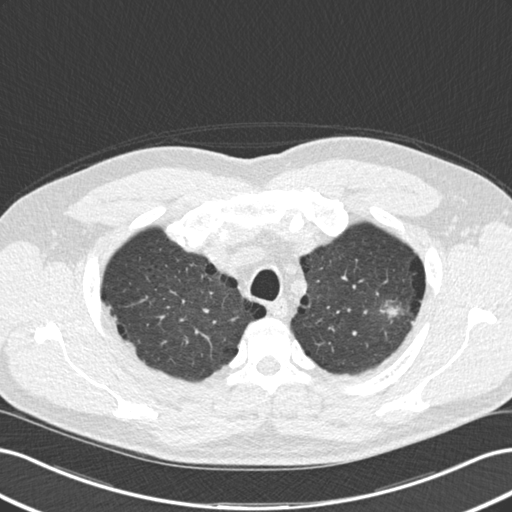
Low-dose screening chest CT, one axial slice. Slice 139 of 177 in the series (ordered by position). Reconstruction kernel B30f. 120 kVp. Lung window (W 1500 / L -600 HU). 2 mm slice thickness. 512 × 512 image matrix.
Outlined on this slice (manually delineated by an expert):
- lesion 1 (tumor, upper lobe of left lung): bounding box (x1, y1, x2, y2) in pixels: (381, 302, 401, 318)